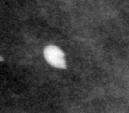
Cropped region of a digitized screen-film mammogram centred on a radiologist-marked abnormality; left breast; MLO view; BI-RADS breast density category 4 (scale 1–4).
- Calcifications, morphology round and regular / lucent center / punctate, distribution diffusely scattered; BI-RADS assessment category 2; benign; no additional work-up was recommended (benign without callback).